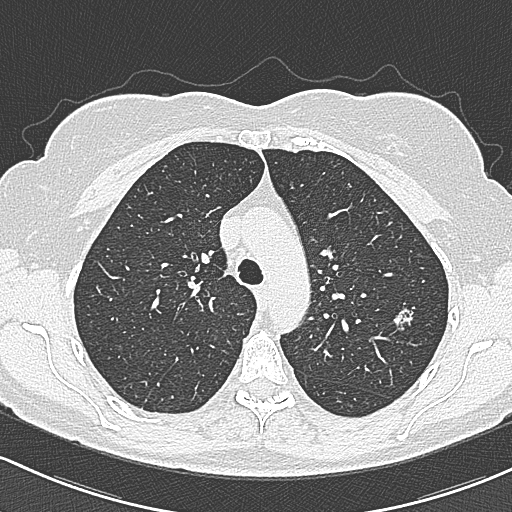
Axial slice from a low-dose chest CT screening exam, first (baseline) screen, lung window (W 1500 / L -600 HU), lung (sharp) reconstruction kernel (B80f), slice 87 of 312 in the series. Female, age 65 years at enrolment. Current smoker at enrolment.
Lesion marked by an expert reader, bounding box [x1, y1, x2, y2] px = [382, 299, 423, 338]. The screening reader recorded 3 non-calcified nodules or masses ≥4 mm on this exam (left upper lobe, left upper lobe, right upper lobe); which of them this box marks is not recorded. Official screen result: positive, change unspecified: nodule(s) >= 4 mm or enlarging nodule(s), mass(es), or other non-specific abnormalities suspicious for lung cancer. Lung cancer was diagnosed 390 days after this screen (after the second annual screen): bronchiolo-alveolar carcinoma, non-mucinous, left upper lobe, stage IA (AJCC 6th edition), 10 mm at pathology.